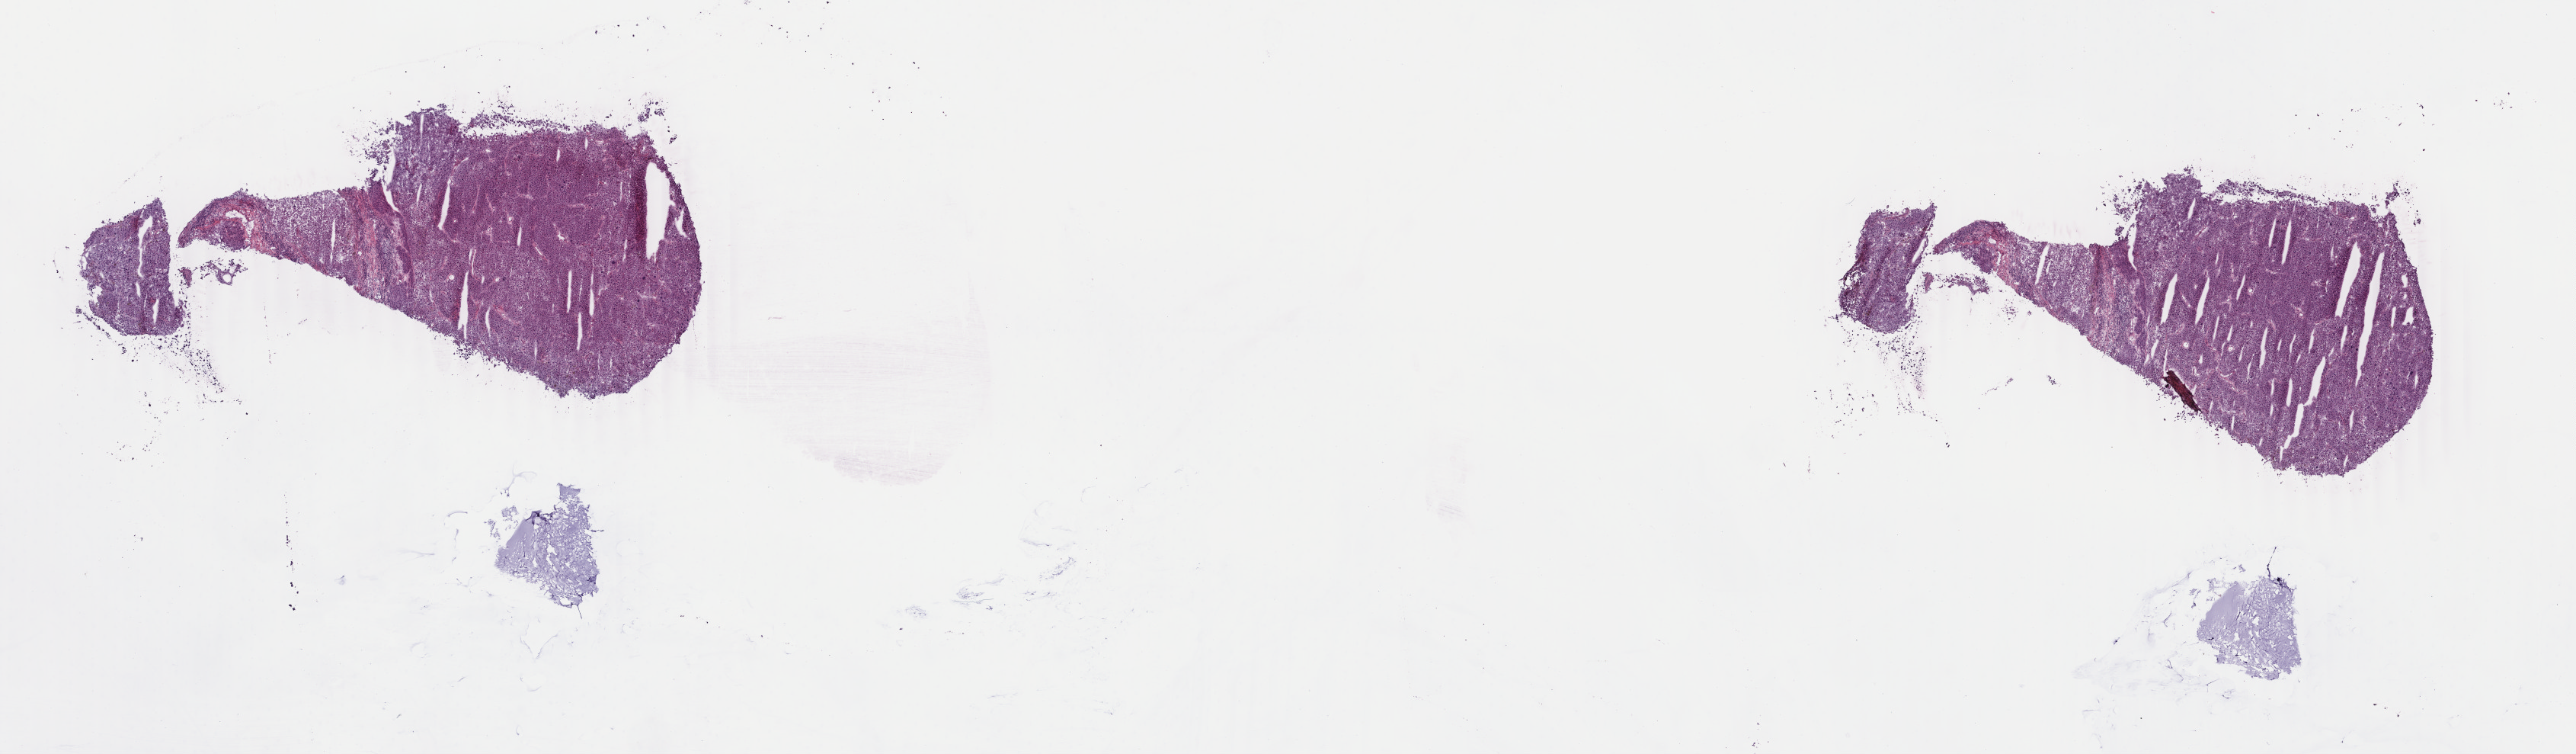
Digitized H&E-stained tissue section (whole slide) — low-resolution overview of the scanned area, about 26.9 x 7.9 mm. Frozen section from the top of the tissue portion. Metastatic tumour sample, sampled site not recorded. Patient: male, age at initial diagnosis 80 years. Slide review estimates, as recorded: tumour cells 100%, tumour nuclei 90%, normal cells 0%, stromal cells 0%, necrosis 0%. Infiltration values recorded for this section: lymphocyte infiltration 0%, monocyte infiltration 0%, neutrophil infiltration 0%.
This section: metastatic tumour tissue. Patient diagnosis: Malignant melanoma, NOS.